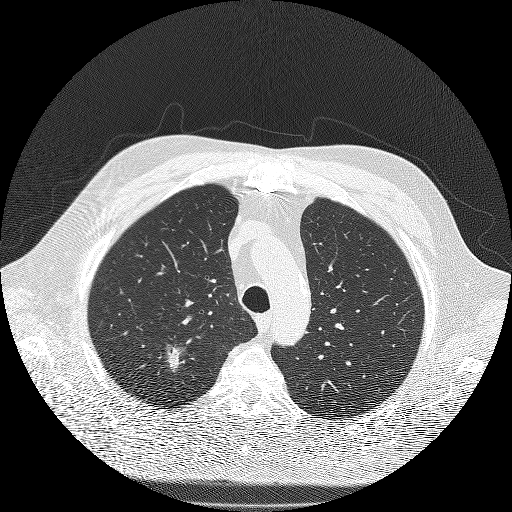
Low-dose screening chest CT, one axial slice. Slice 149 of 180 in the series (ordered by position). Reconstruction kernel FC51. Lung window (W 1500 / L -600 HU). 2 mm slice thickness. 512 × 512 image matrix, field of view 385 × 385 mm.
Annotated regions visible in this slice (outlined manually by an expert reader):
- lesion 1 (tumor, upper lobe of right lung): bounding box (x1, y1, x2, y2) in pixels: (167, 346, 185, 372)